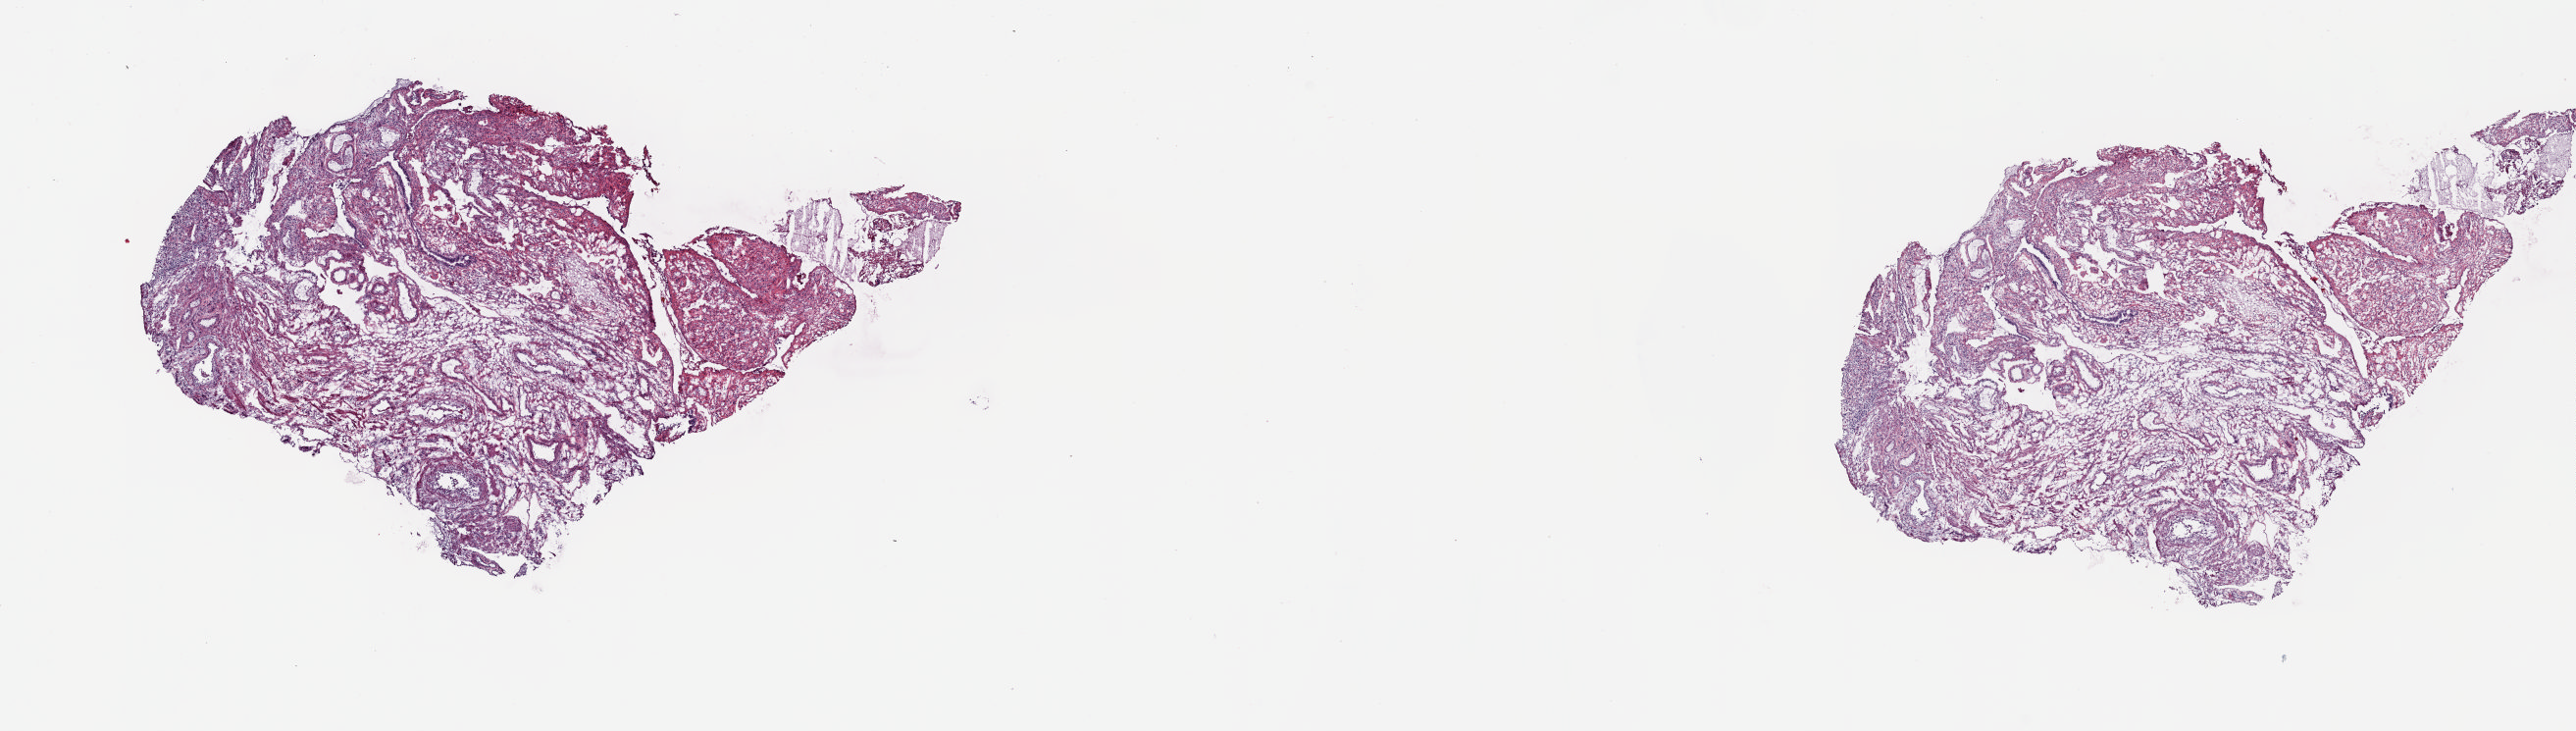
Hematoxylin and eosin (H&E) stained whole-slide image, a low-resolution overview of the entire scanned area, about 20.8 x 5.9 mm; frozen section; sample: solid tissue normal (non-tumour tissue), uterus. Patient: female, age at initial diagnosis 56 years. Slide review estimates, as recorded: tumour cells 0%, tumour nuclei 0%, normal cells 100%, stromal cells 0%, necrosis 0%. Inflammatory infiltration, as recorded: lymphocyte infiltration 3%, monocyte infiltration 6%, neutrophil infiltration 1%.
This section: solid tissue normal sample (biorepository sample class). Patient diagnosis: Leiomyosarcoma, NOS.